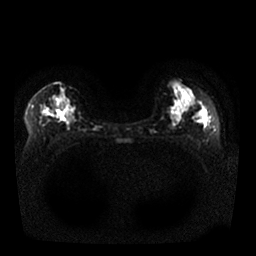
Breast MRI, one axial slice. Diffusion-weighted series; image 2 of 4 stored at this slice position (different b-values; order by instance number). 1.5 T. 256 × 256 image matrix, field of view 340 × 340 mm. Female patient.
Annotated regions visible in this slice (manually delineated by an expert):
- tumour on diffusion-weighted imaging: bounding box <42,110,57,118> (left, top, right, bottom; pixels)